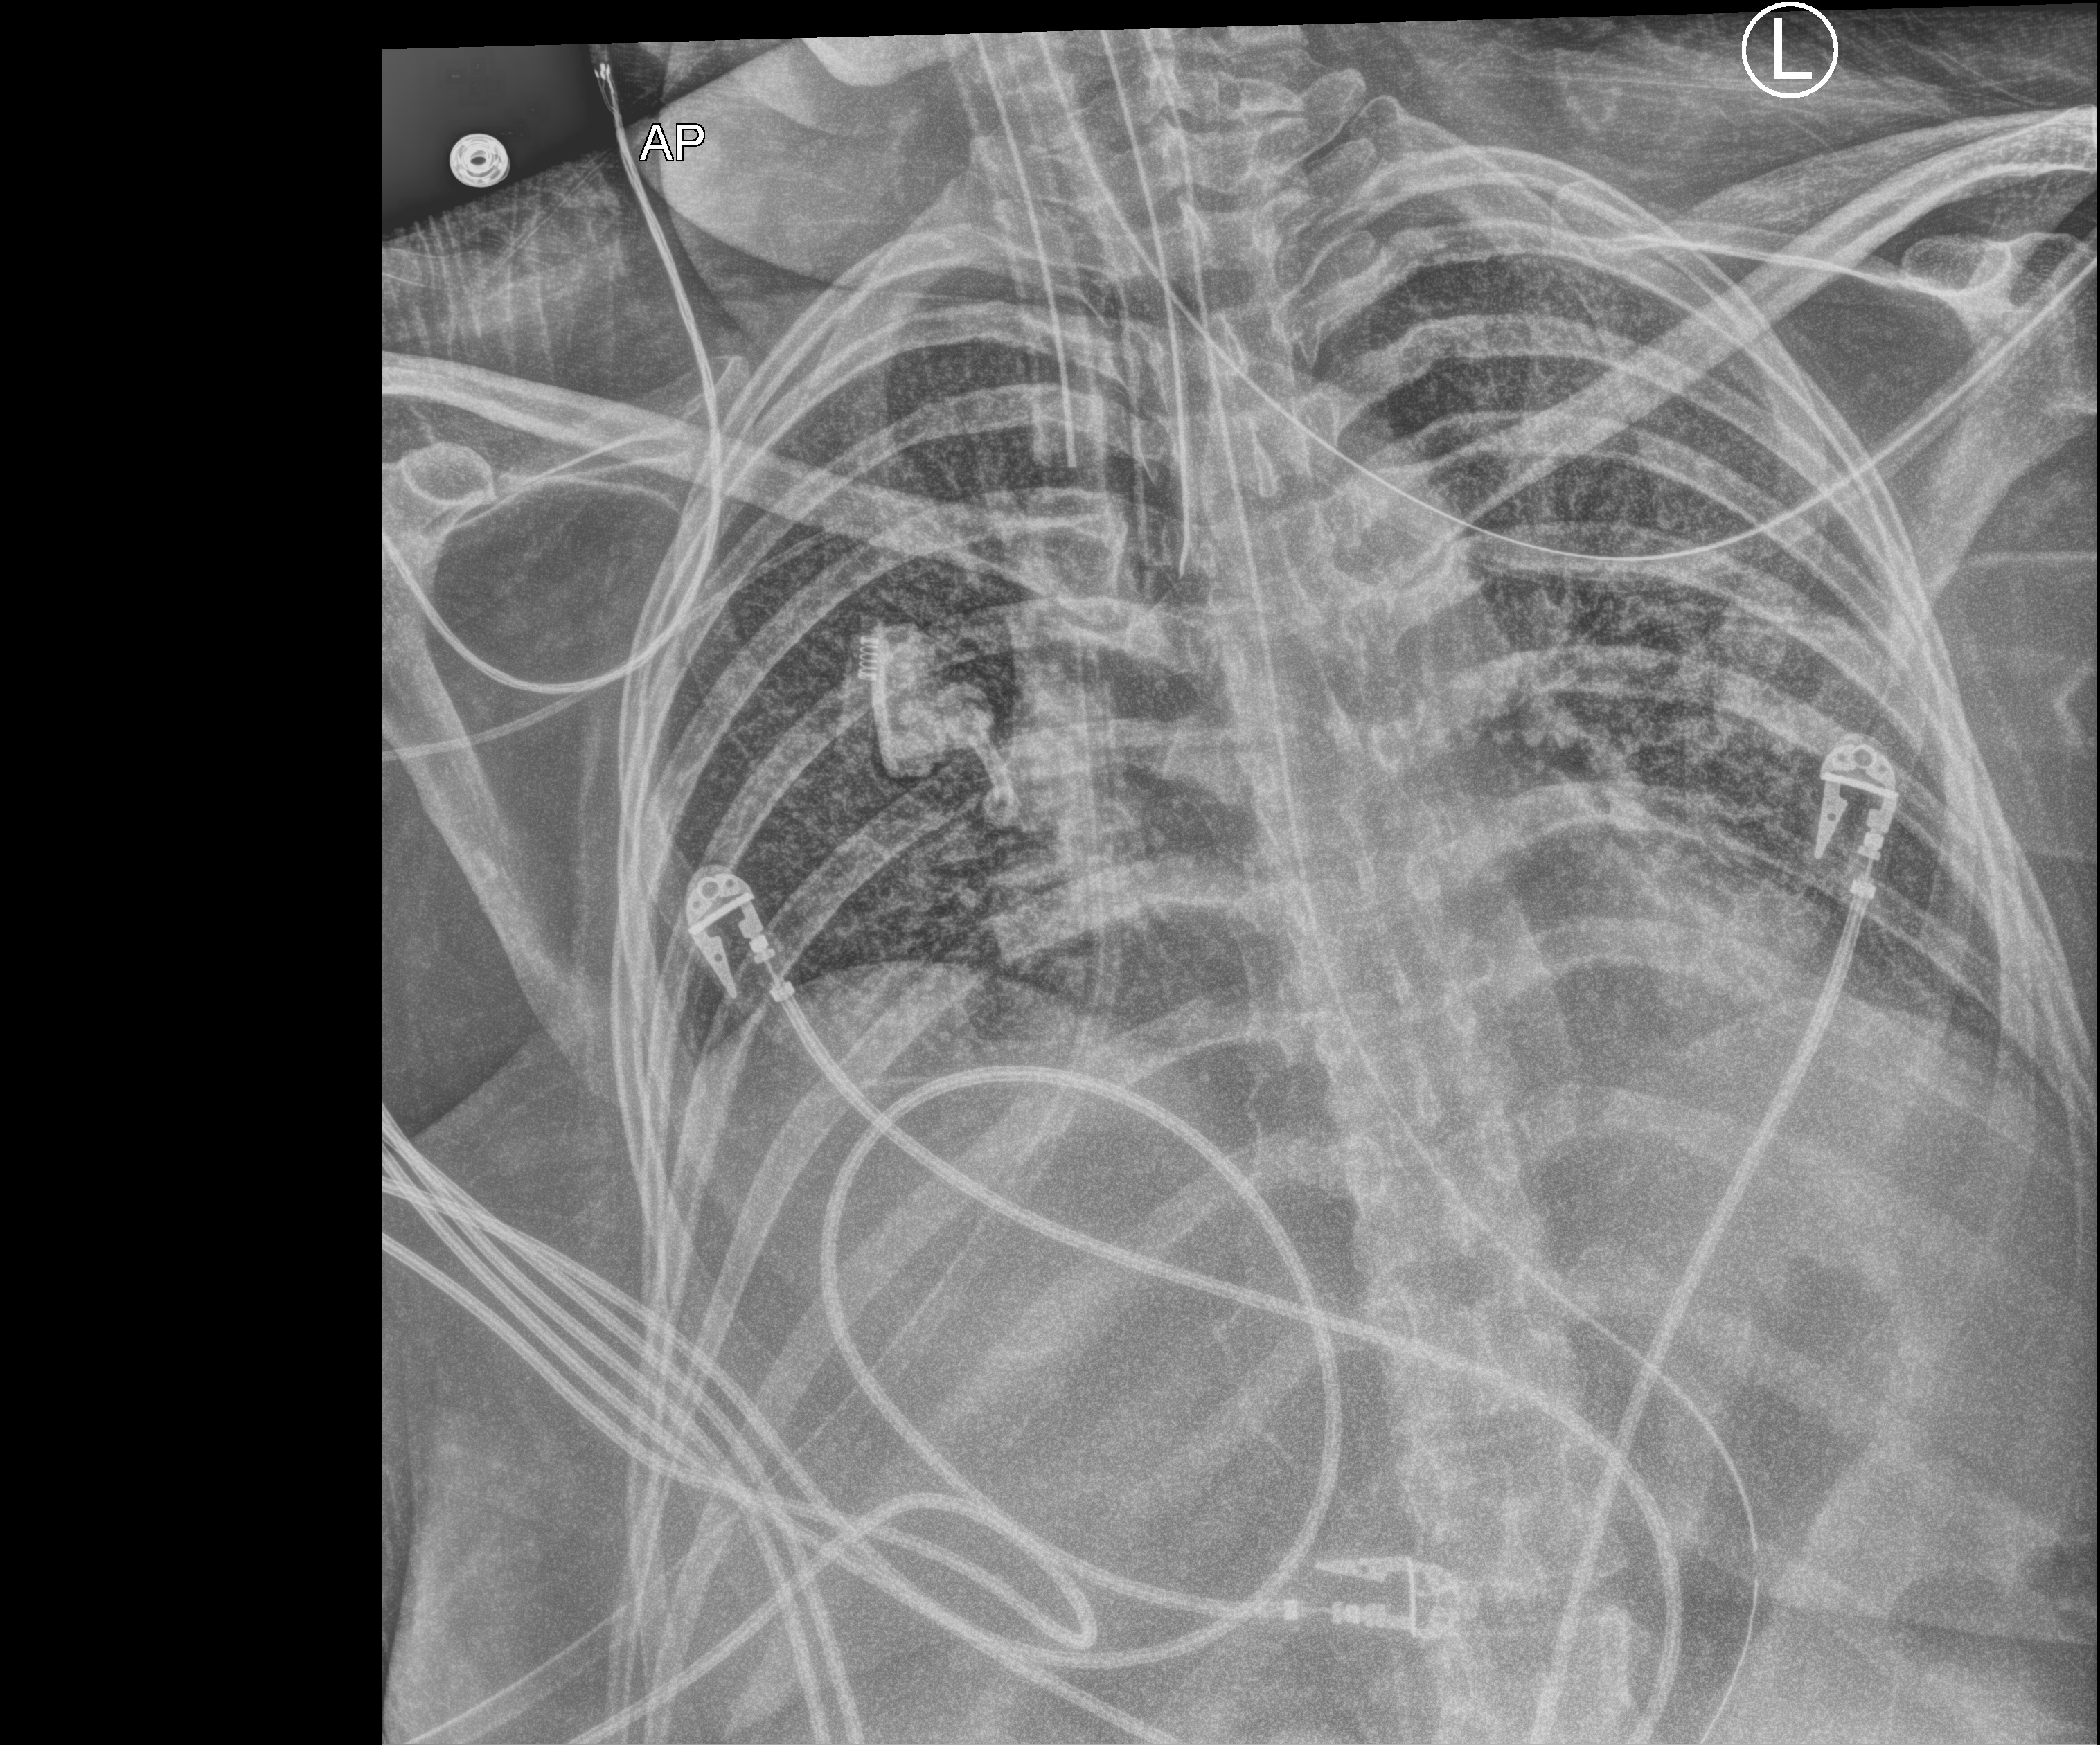
Chest X-ray (portable); anteroposterior (AP) projection. Patient hospitalised with COVID-19; female, aged 18–59 years.
Admission-level facts for this patient (not findings on this image; timing relative to this image not recorded):
- admitted to intensive care during this hospital stay: yes
- smoking status (admission record): former